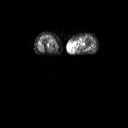
FDG PET of an extremity soft-tissue mass (from a PET/CT study), one axial slice; slice 7 of 91 in the series (ordered by position); 128 × 128 image matrix, field of view 700 × 700 mm. Female patient, age 74 years. From the clinical record (not read from this slice): histological type: pleomorphic leiomyosarcoma; grade: high; site of the primary tumour: left thigh.
Annotated regions visible in this slice (expert contour drawn on MRI and transferred to this co-registered scan by the dataset authors):
- gross tumour volume including surrounding oedema: bounding box [x1, y1, x2, y2] px = [72, 38, 87, 50]